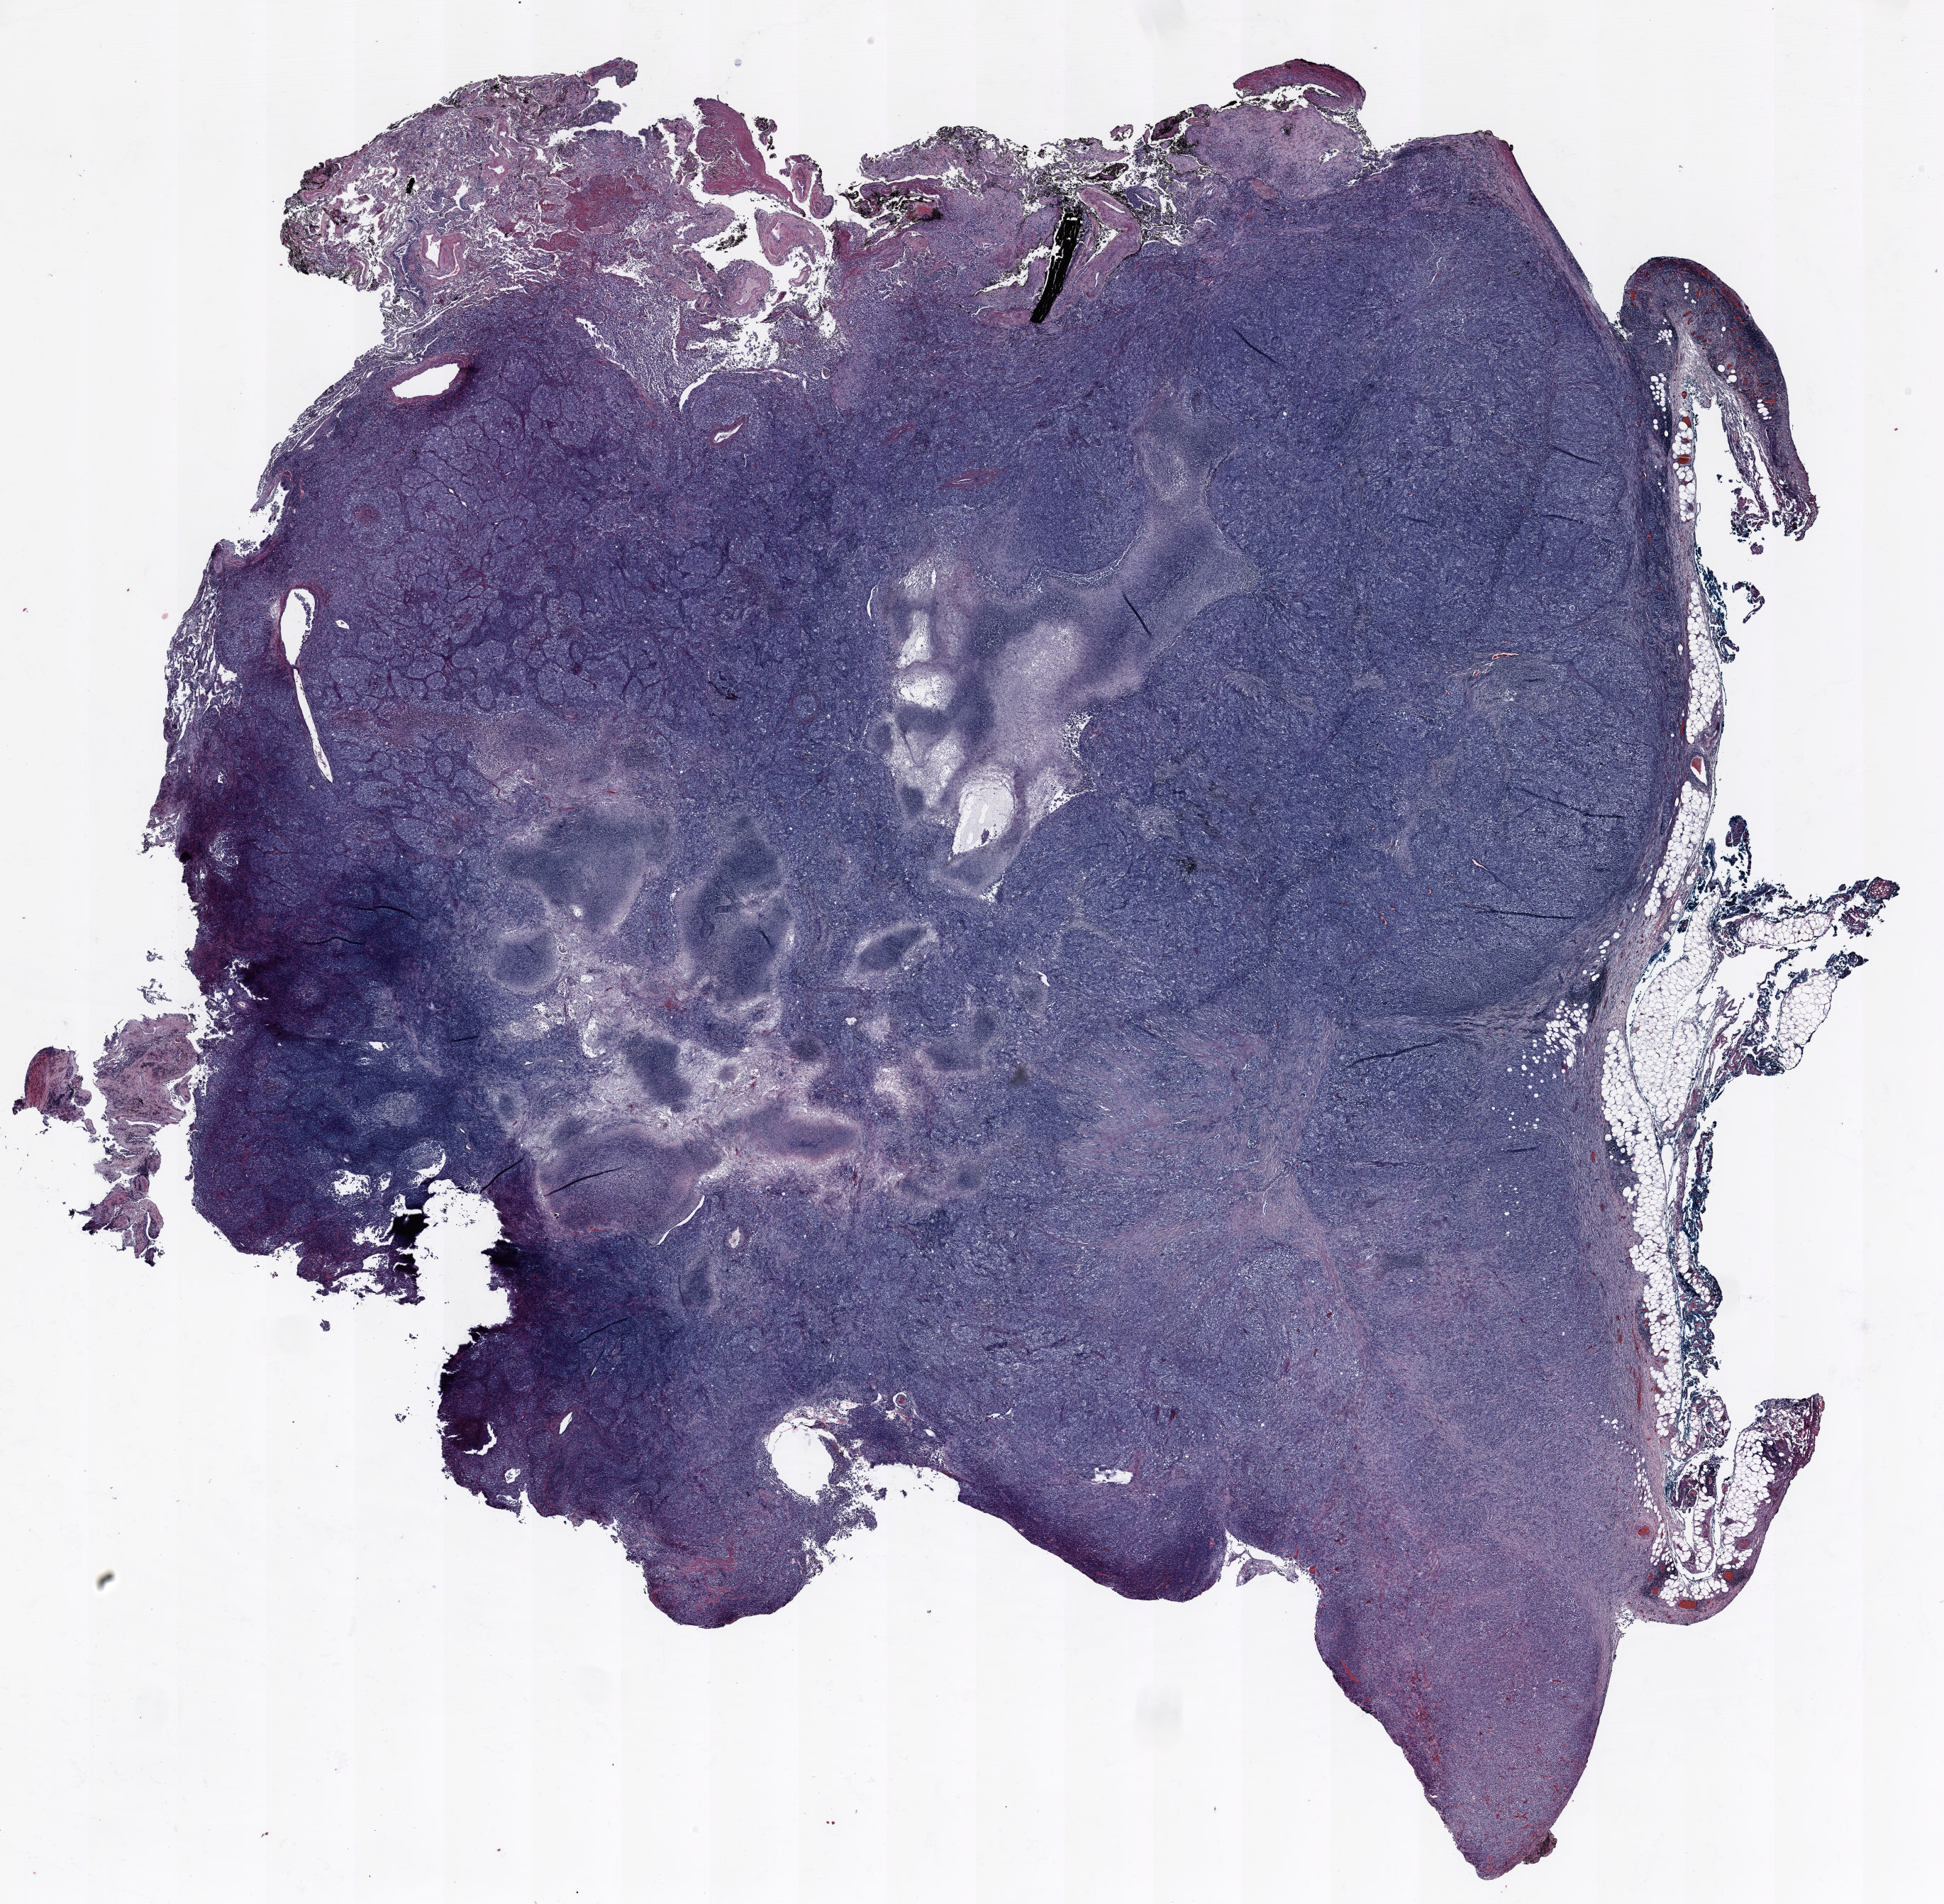
H&E whole-slide image, shown as a low-resolution overview of the whole scanned area (about 22.0 x 21.6 mm); formalin-fixed paraffin-embedded (FFPE) section; lung tissue. Male, age 63 at enrolment. Current smoker at enrolment. Grade: undifferentiated (G4).
ICD-O-3 topography: upper lobe of lung (C34.1). Participant's lung-cancer diagnosis: Large cell carcinoma, NOS. Tumour size (pathology): 30 mm. Stage (AJCC 6th edition): IIIB. Primary tumour location (clinical record): left upper lobe.